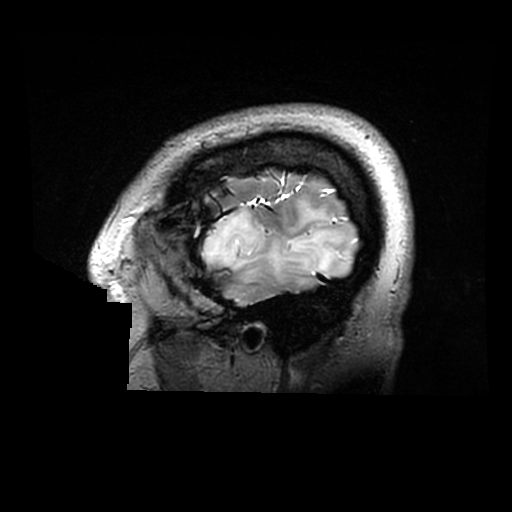
Brain MRI from a brain-tumour surgery series, one sagittal slice. Slice 251 of 320 in the series (ordered by position). 512 × 512 image matrix. Case-level facts recorded for this patient, not image findings: histopathology: Astrocytoma; WHO grade: 2; IDH mutation: yes.
Outlined on this slice (expert manual segmentation):
- tumour: bounding box <199,202,348,284> (left, top, right, bottom; pixels)